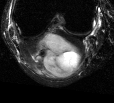
MRI of an extremity soft-tissue mass, one axial slice. Slice 15 of 44 in the series (ordered by position). T2-weighted fat-saturated. MR volume resampled by the dataset authors to the PET/CT grid (not the native acquisition matrix). 114 × 103 image matrix. Female patient. From the clinical record (not read from this slice): histological type: liposarcoma; site of the primary tumour: right thigh.
Annotated regions visible in this slice (expert contour drawn on MRI and transferred to this co-registered scan by the dataset authors):
- gross tumour volume (mass): bounding box [x1, y1, x2, y2] px = [31, 32, 80, 78]